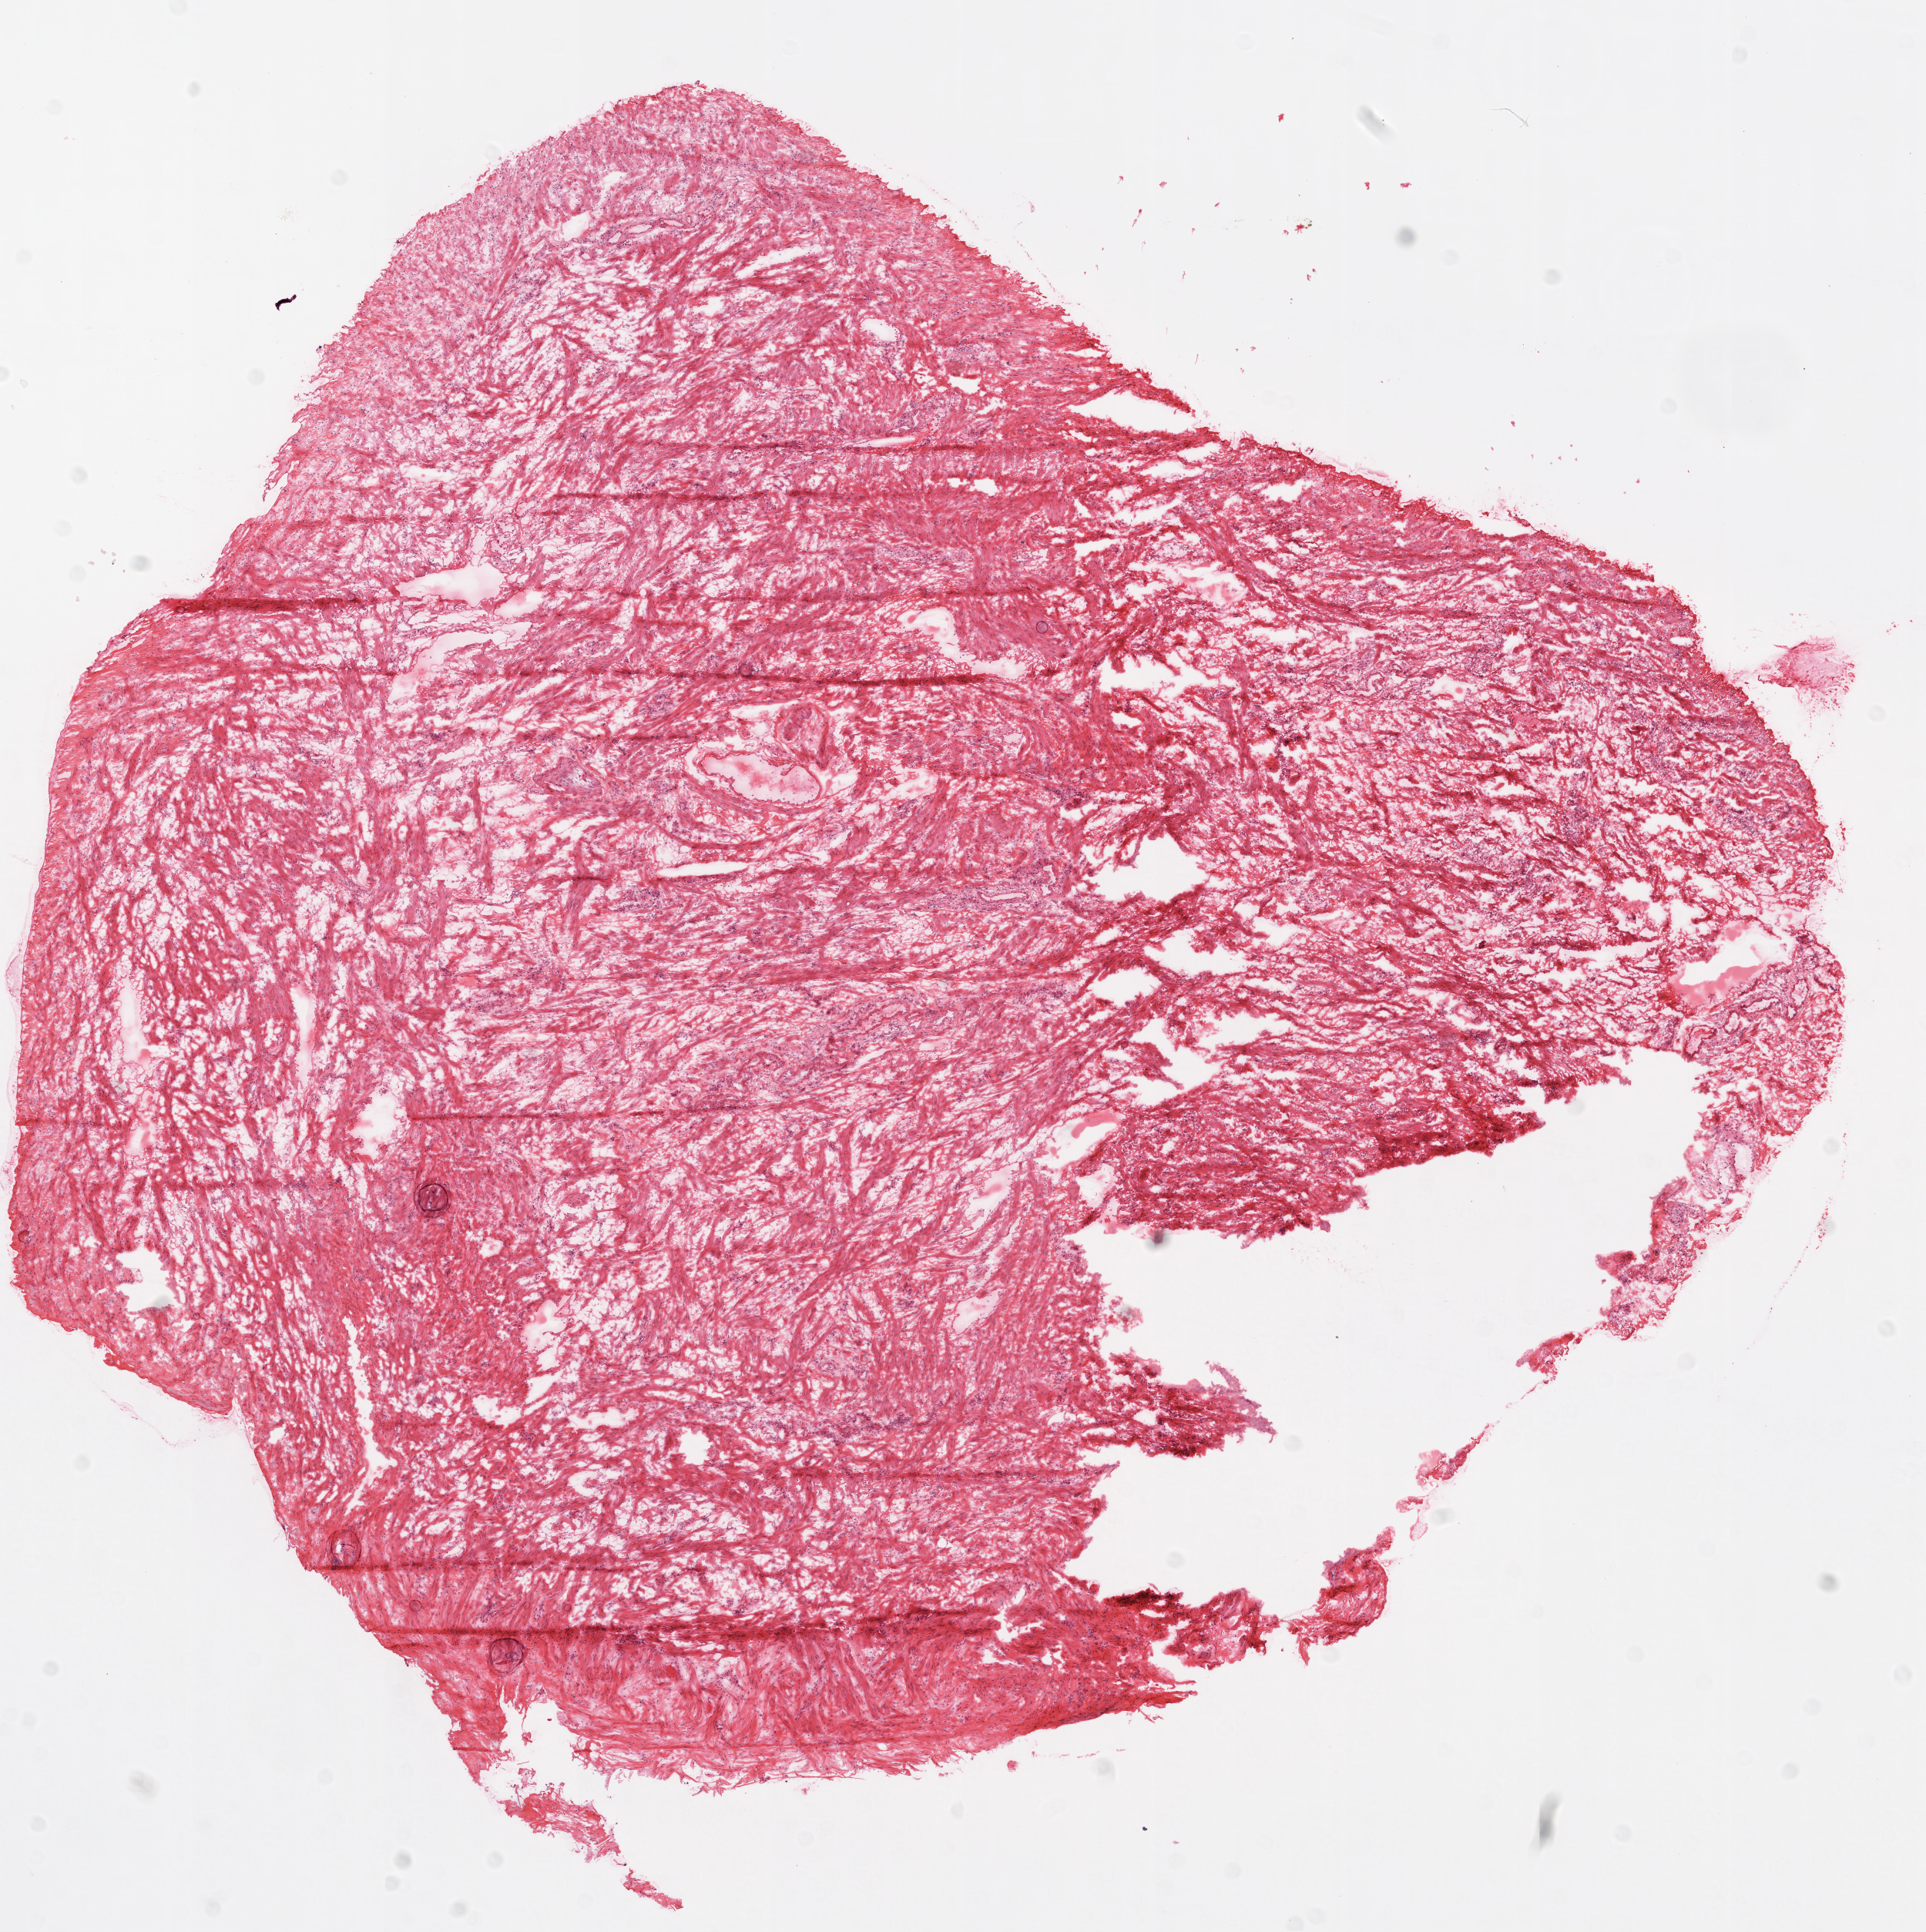
Whole-slide histology image, H&E-stained — low-resolution overview of the scanned area, about 10.0 x 10.1 mm, frozen section from the top of the tissue portion, sample: solid tissue normal (non-tumour tissue), ovary. Female, age 40 years at initial diagnosis.
This section: solid tissue normal (non-tumour) sample from the same patient. Patient diagnosis: Serous cystadenocarcinoma, NOS.